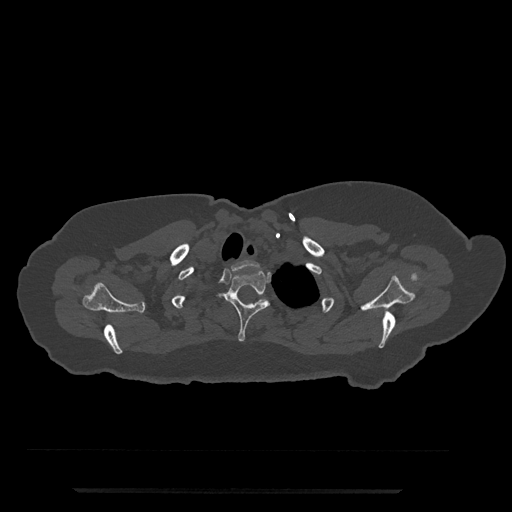
CT including the spine, one axial slice; position 672 of 797 along the scan axis; bone window (W 1800 / L 400 HU); 512 × 512 image matrix, field of view 440 × 440 mm. Patient: female, 51 years. From the clinical record (not read from this slice): primary cancer: neuro.
Annotated regions visible in this slice (semi-automatic segmentation, software-assisted and operator-edited):
- T1 vertebra: box from (x=231, y=260) to (x=259, y=271) px
- T2 vertebra: (x=219, y=271)–(x=270, y=342)
- T3 vertebra: (x=258, y=298)–(x=267, y=302)